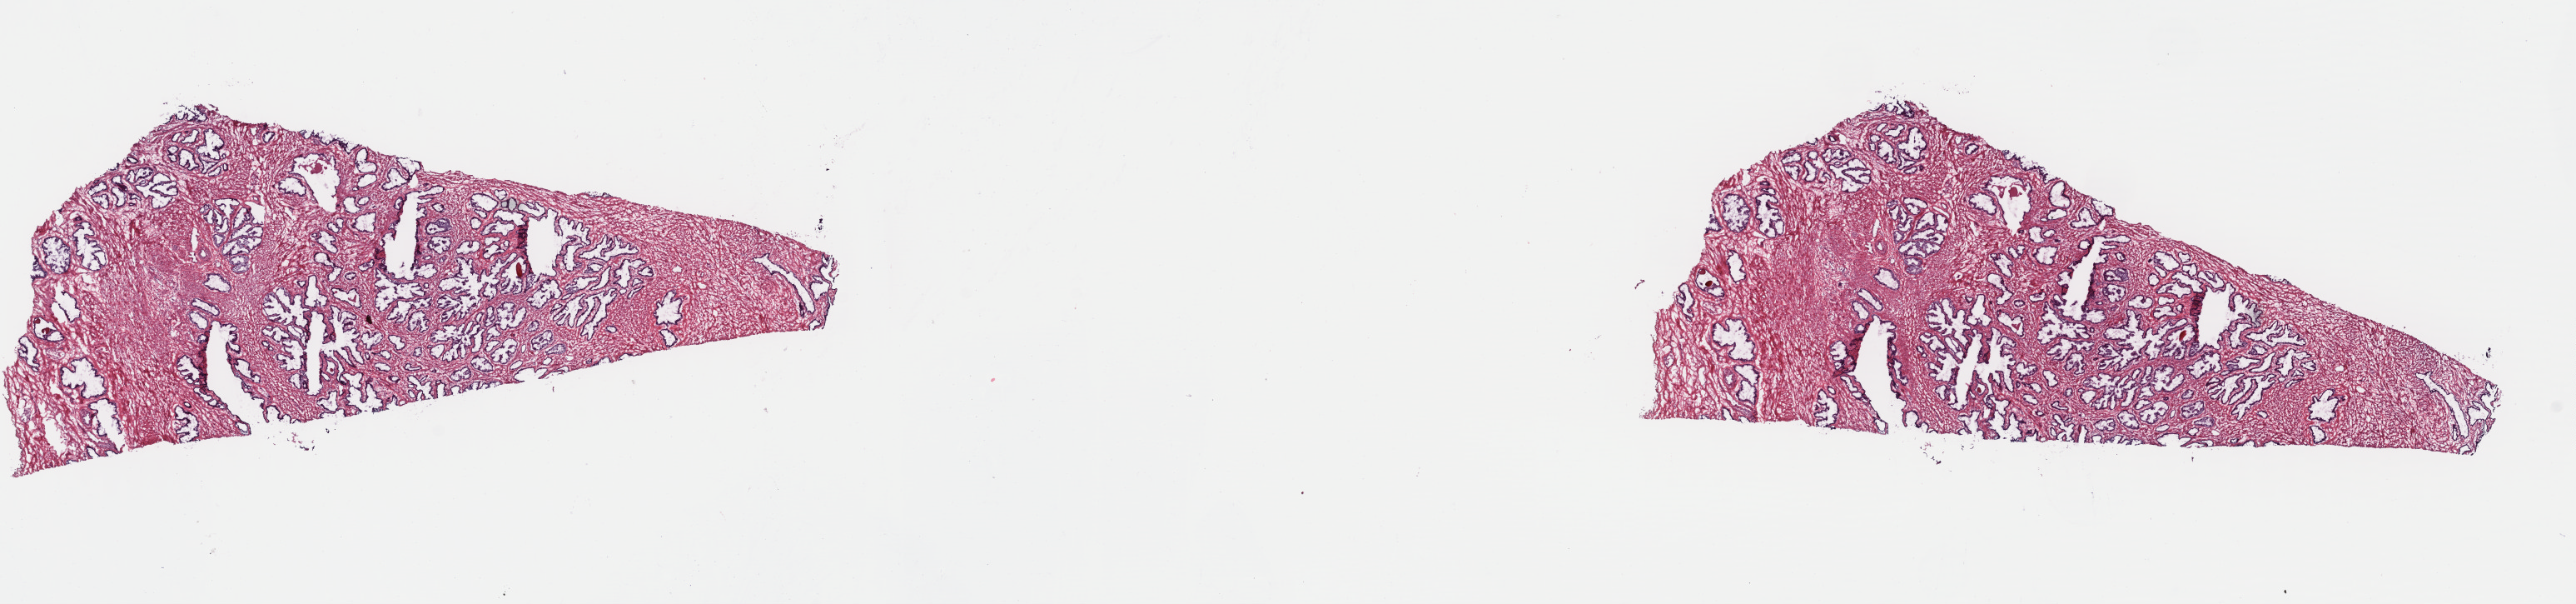
Whole-slide histology image, Hematoxylin and eosin (H&E) stained — shown as a low-resolution overview of the whole scanned area (about 24.4 x 5.7 mm, acquisition: 40x scan); frozen section; prostate, primary tumour sample. Male patient; age at initial diagnosis 55 years. Gleason score: 7 (3+4). Pathologist review of this section (percent, as recorded): tumour cells 80%, tumour nuclei 70%, normal cells 20%, stromal cells 0%, necrosis 0%. Infiltration values recorded for this section: lymphocyte infiltration 2%, monocyte infiltration 0%, neutrophil infiltration 0%.
Histologic diagnosis: Adenocarcinoma, NOS (prostate gland). Laterality: bilateral.